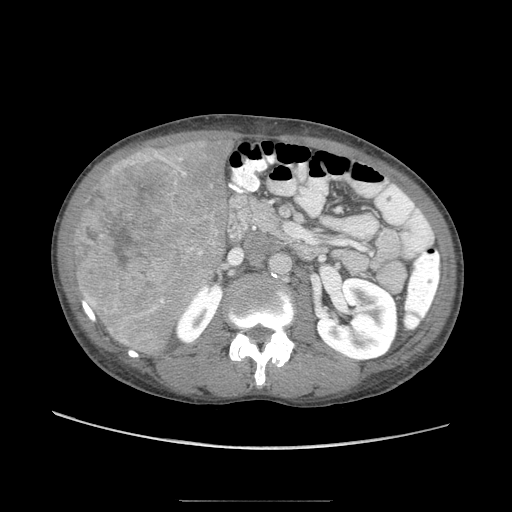
Contrast-enhanced abdominal CT (liver protocol), one axial slice. Position 27 of 103 along the scan axis. 120 kVp. Soft-tissue window (W 400 / L 40 HU). 2.5 mm slice thickness. 512 × 512 image matrix, field of view 380 × 380 mm. From the clinical record (not read from this slice): diagnosis: hepatocellular carcinoma (patient treated with transarterial chemoembolisation; whether this scan precedes or follows treatment is not stated here); TNM stage (as recorded): Stage-IIIA; Child-Pugh class: A; tumour nodularity: multinodular.
Structures marked on this image (semi-automatically segmented with operator editing):
- liver parenchyma outside the tumour (the mass and vessels are separate outlines, so this box may not span the whole liver): bounding box <90,132,234,356> (left, top, right, bottom; pixels)
- mass: <69,147,213,335>
- liver vessels: <125,156,156,321>